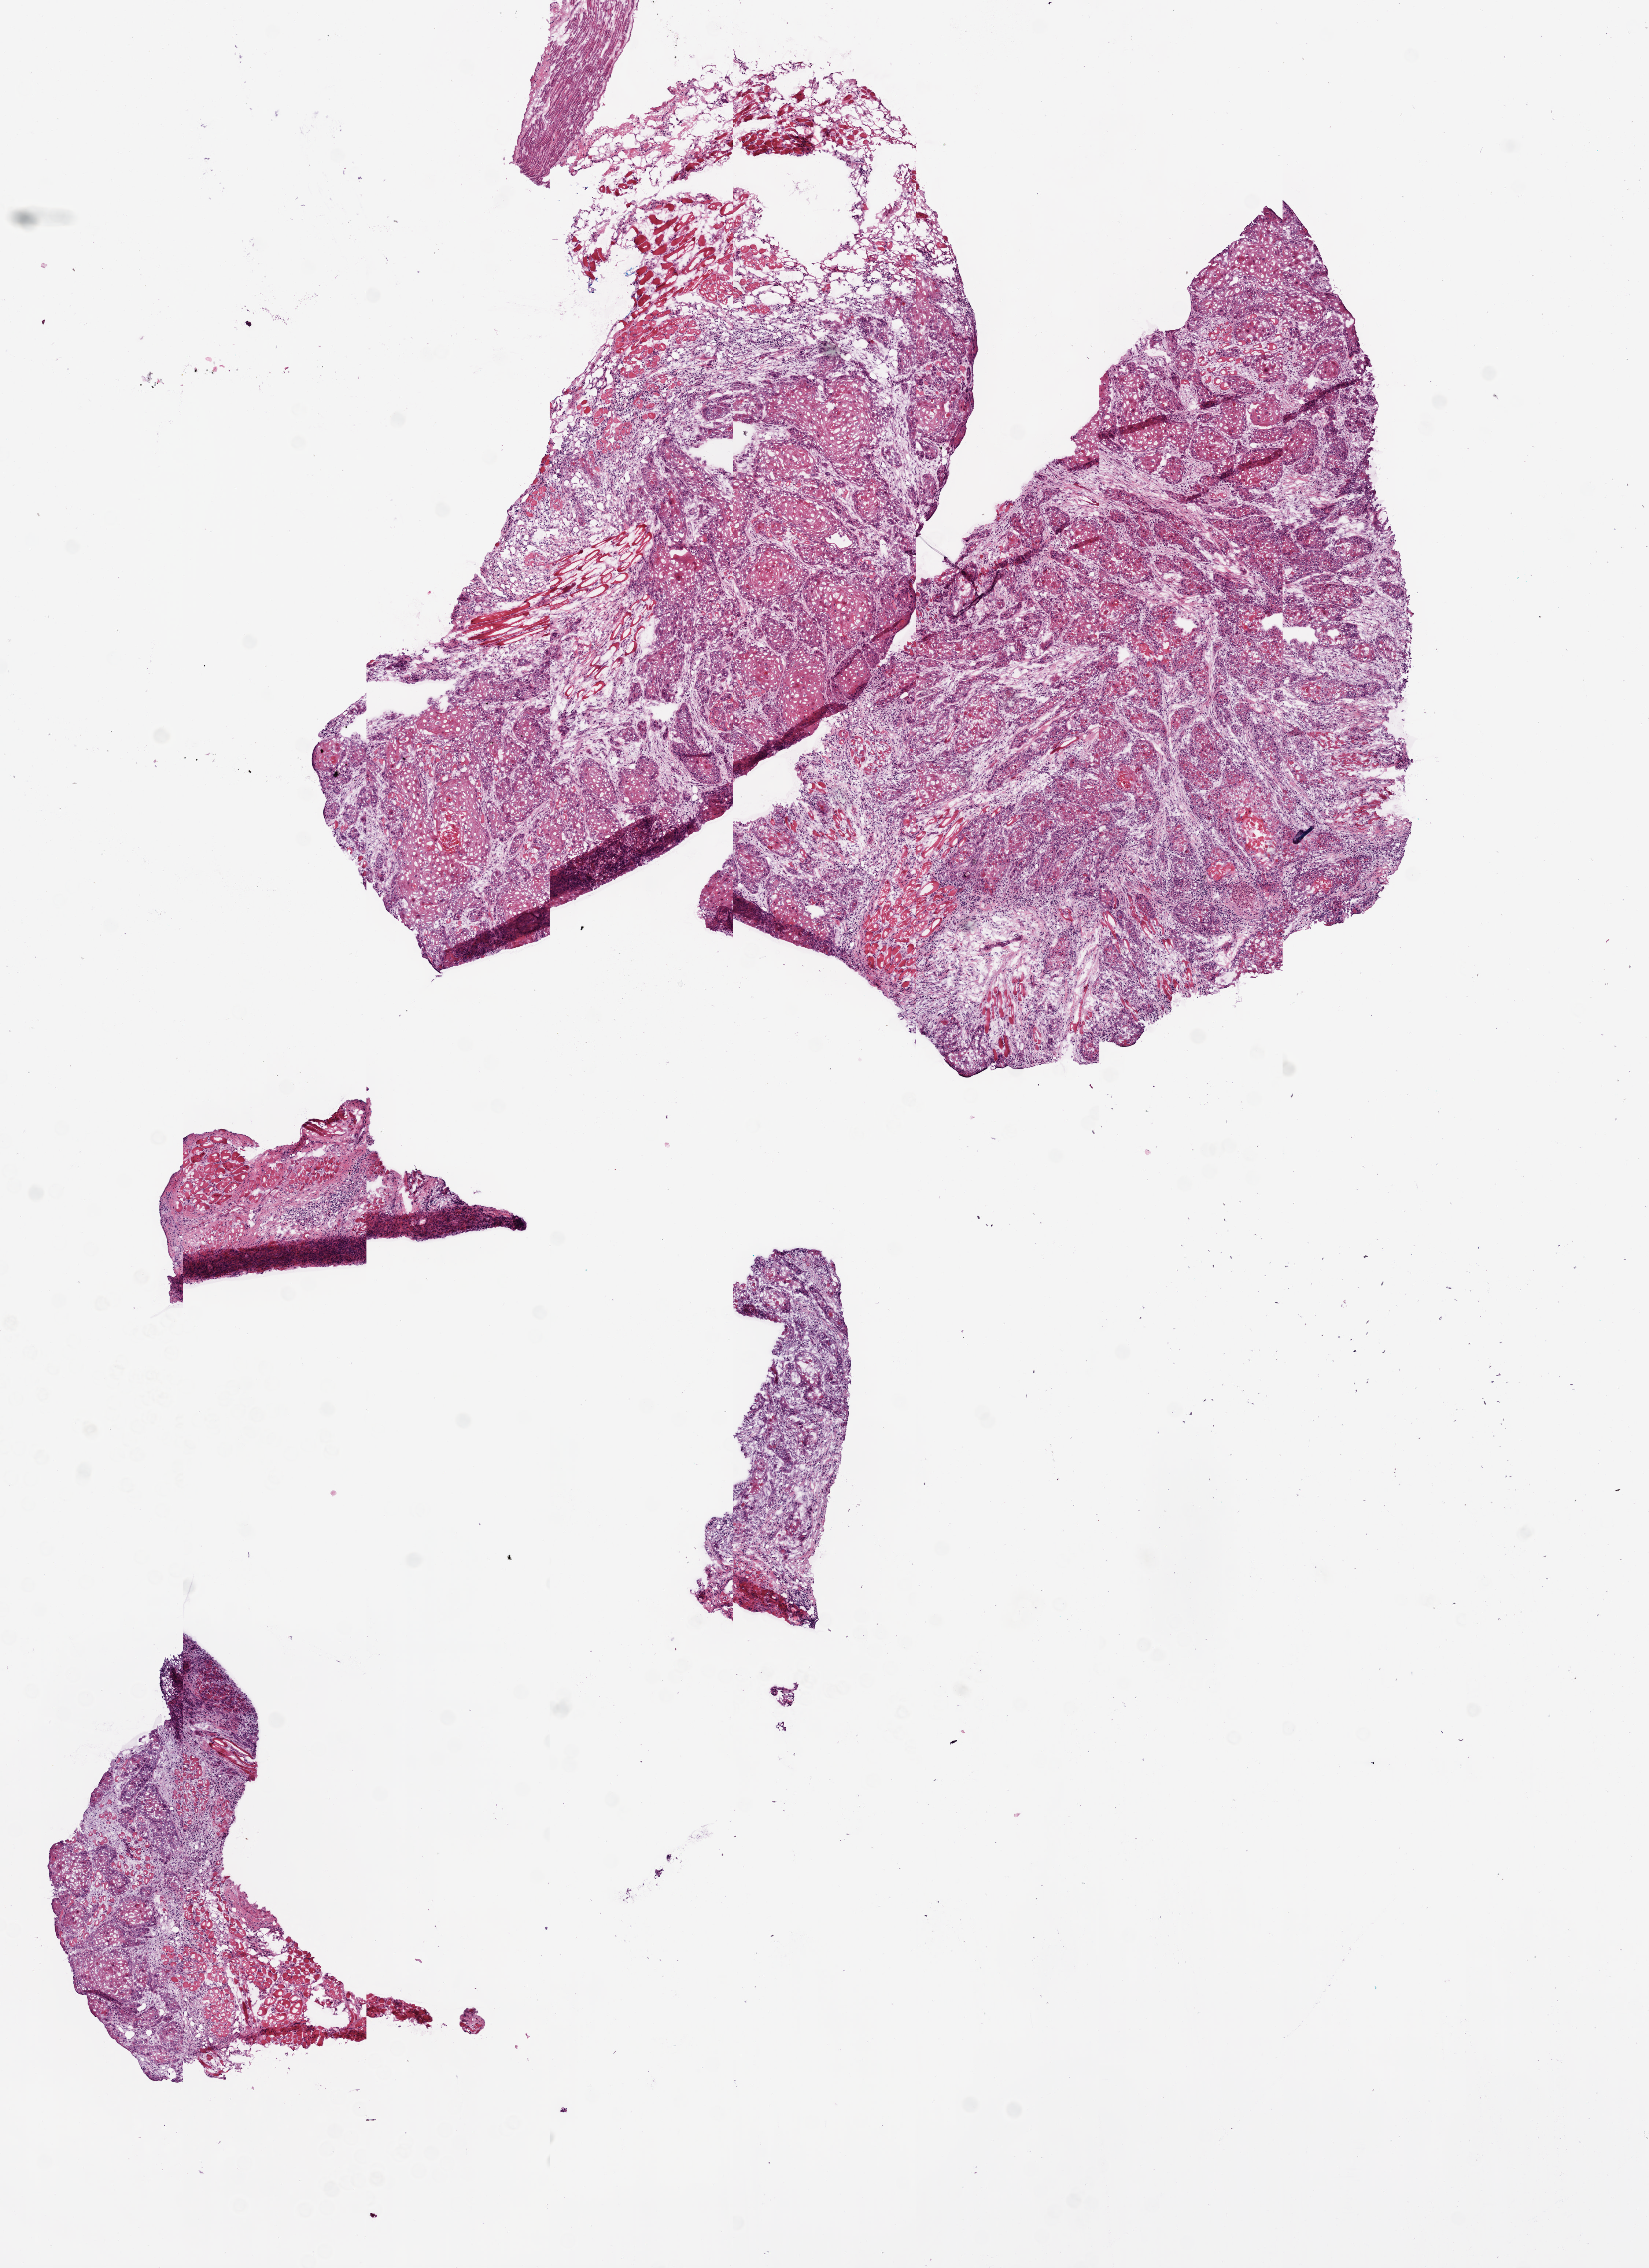
Digitized H&E tissue section (whole slide) — whole scanned area (about 9.0 x 12.4 mm, acquisition: 20x scan) shown as a low-resolution overview, frozen section from the bottom of the tissue portion, primary tumour sample from the head and neck. Female, age 70 years at initial diagnosis. Histologic grade: G2 (moderately differentiated). Pathologist review of this section (percent, as recorded): tumour cells 82%, tumour nuclei 75%, normal cells 0%, stromal cells 15%, necrosis 3%.
Pathologic diagnosis: Squamous cell carcinoma, NOS.